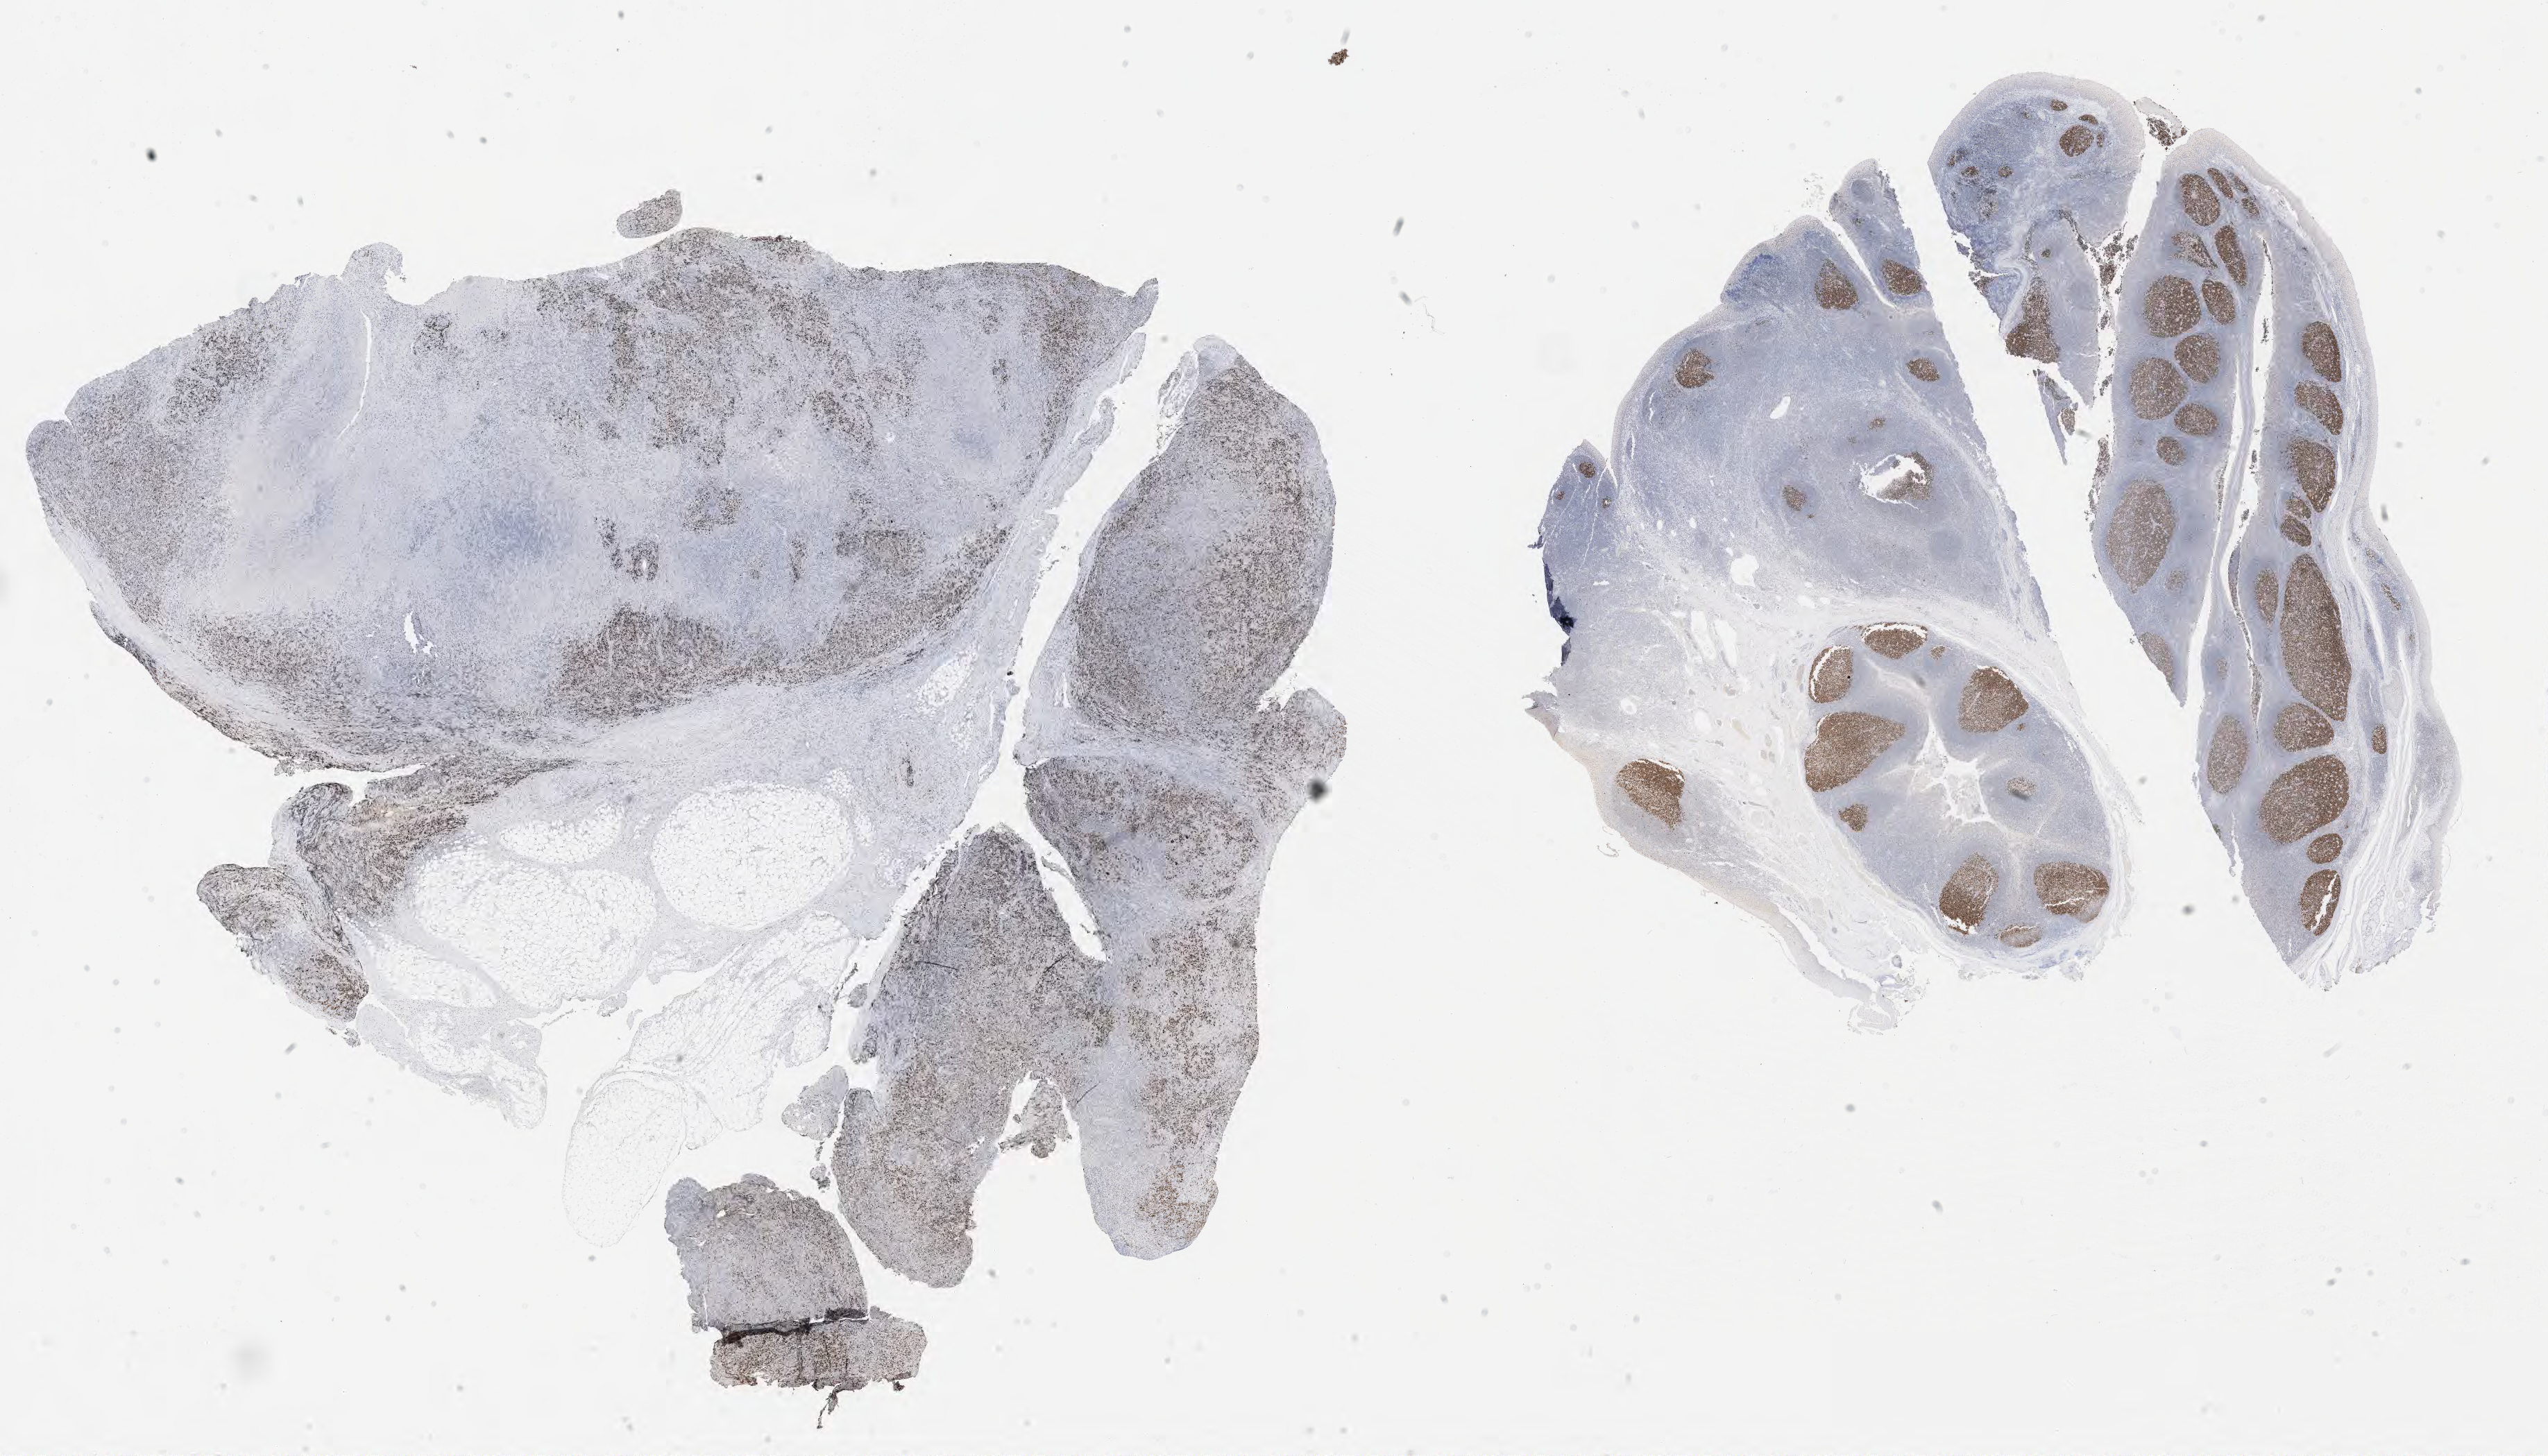
IHC for BCL6, whole-slide image — low-resolution overview of the scanned area, about 29.7 x 17.0 mm. Tumor tissue. Patient female; 46 years old.
- diagnosis: Diffuse large B-cell lymphoma, NOS